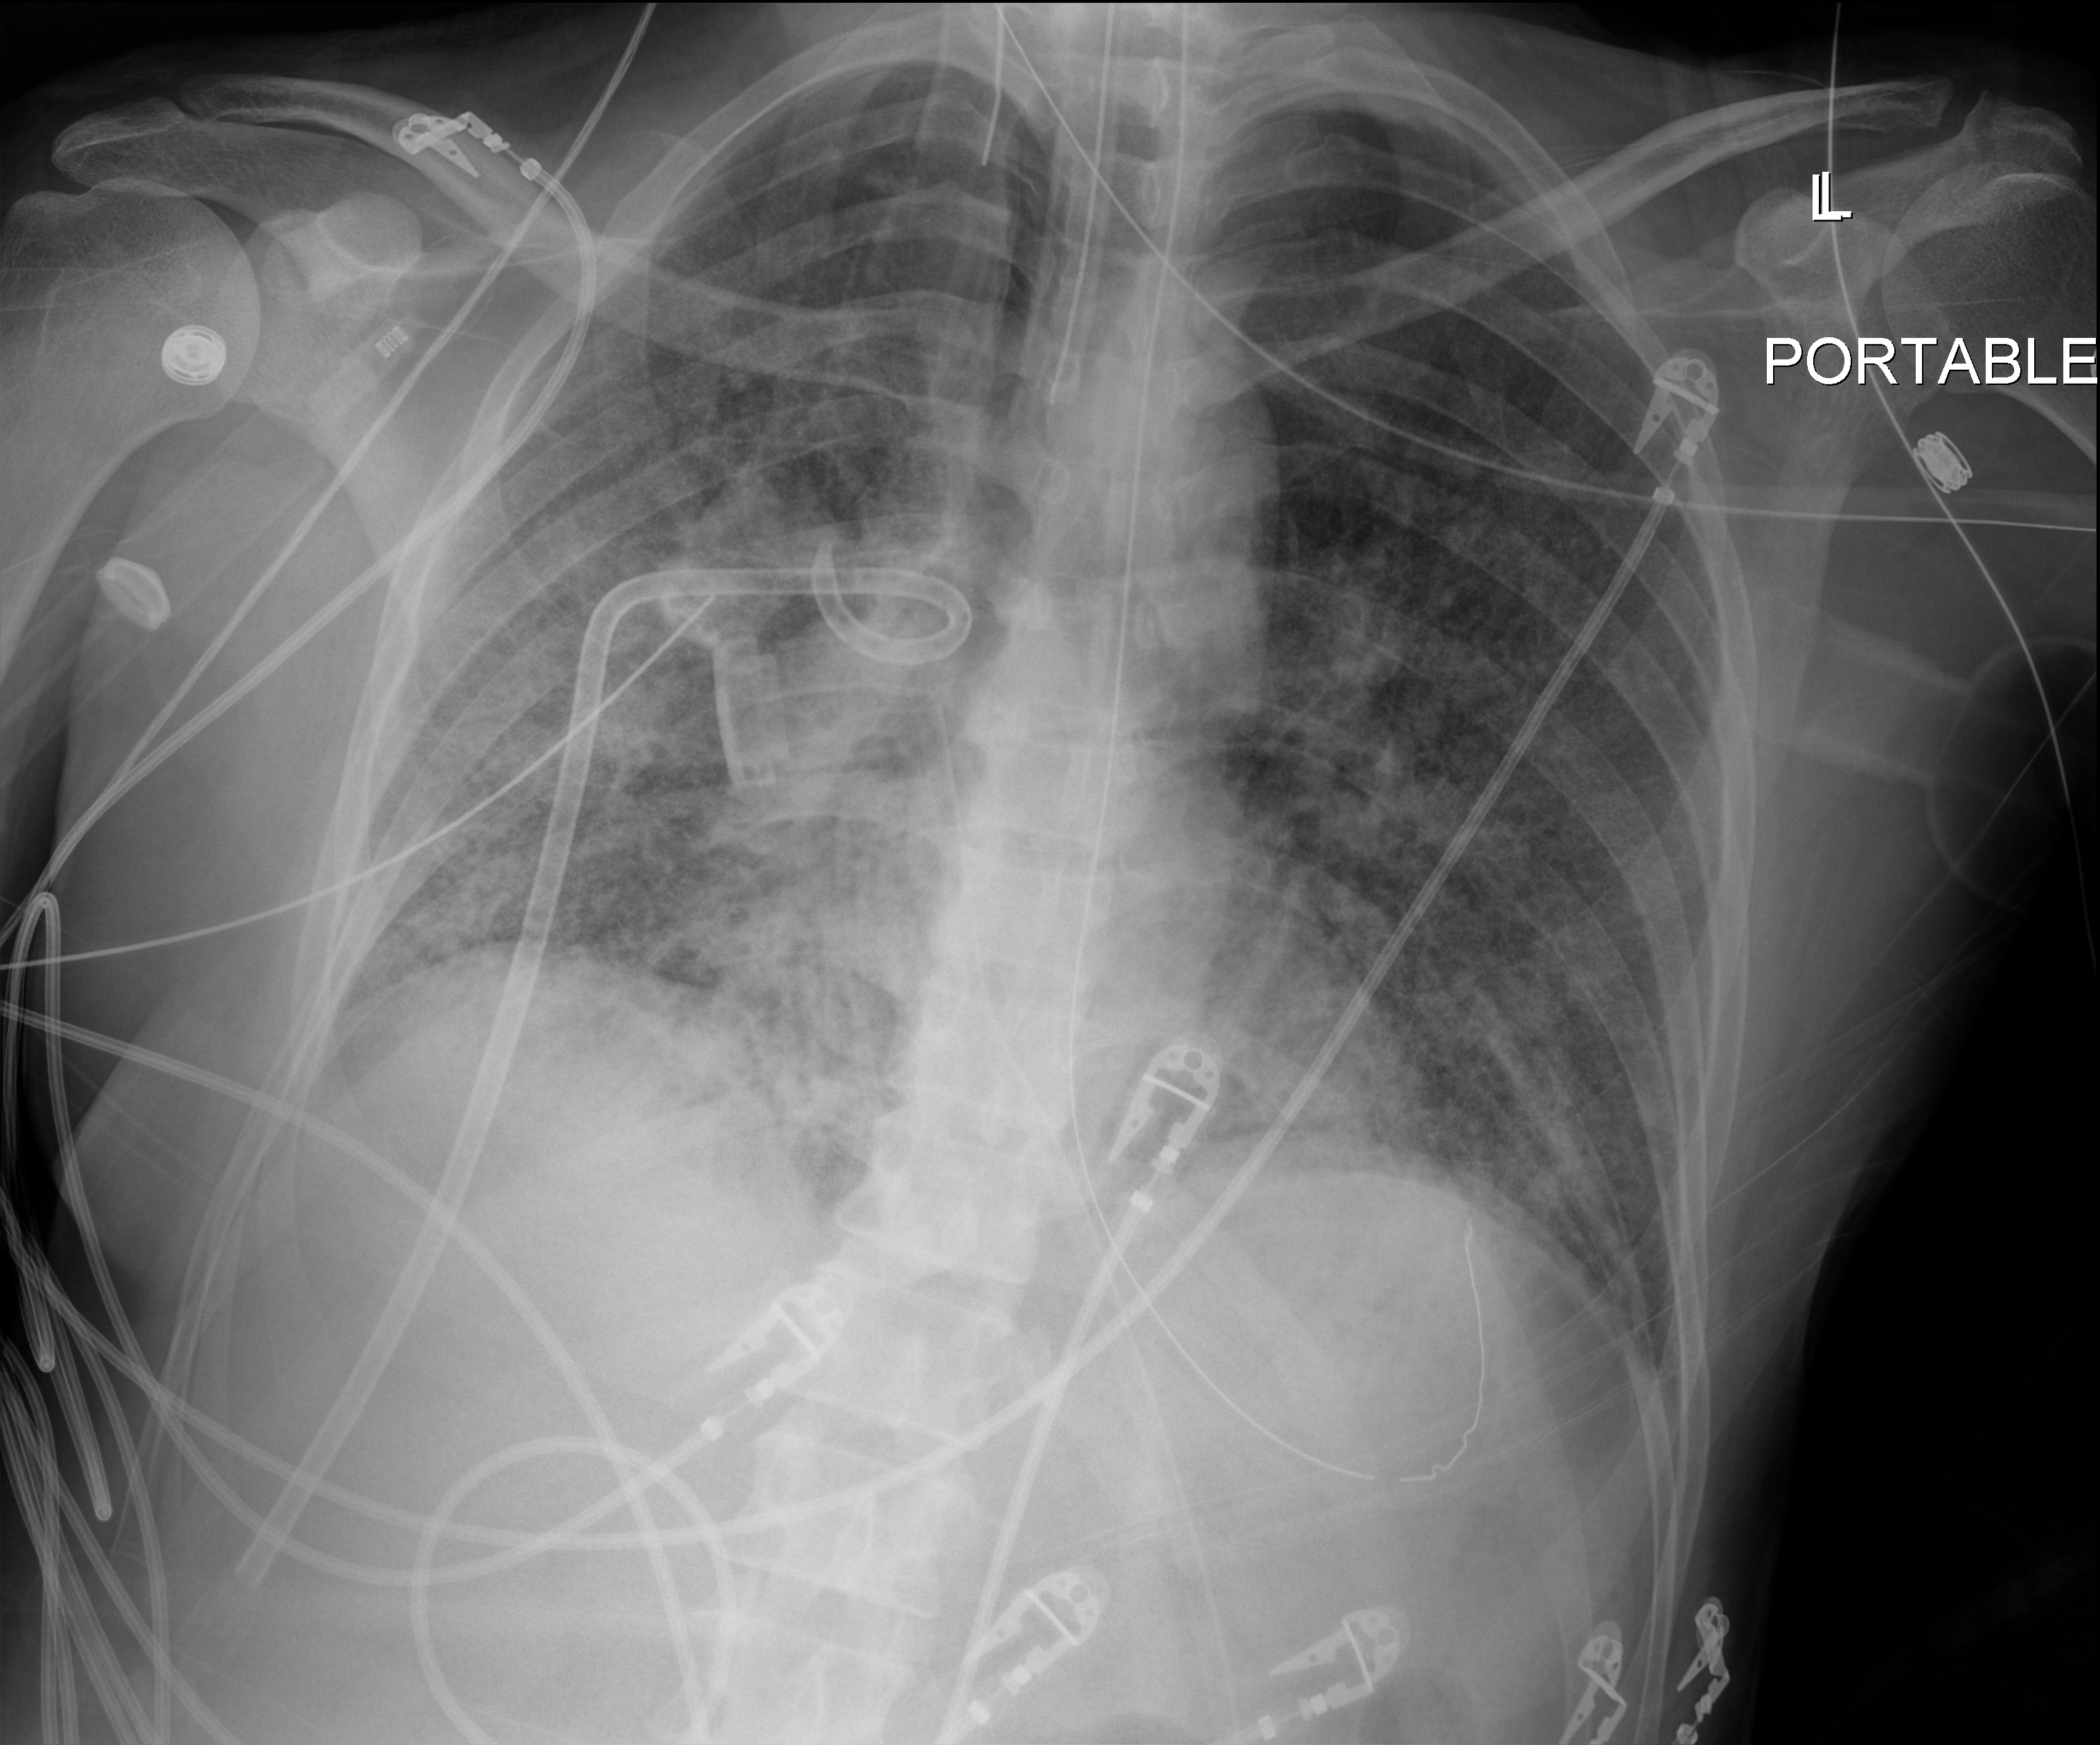
Chest radiograph (digital radiography); anteroposterior (AP) projection. Adult patient hospitalised with COVID-19, age 18–59 years.
From the hospital-stay record, not from the radiograph (when in the stay this image was taken is not recorded):
- length of hospital stay: 41 days
- mechanically ventilated during this hospital stay: yes
- admitted to intensive care during this hospital stay: yes